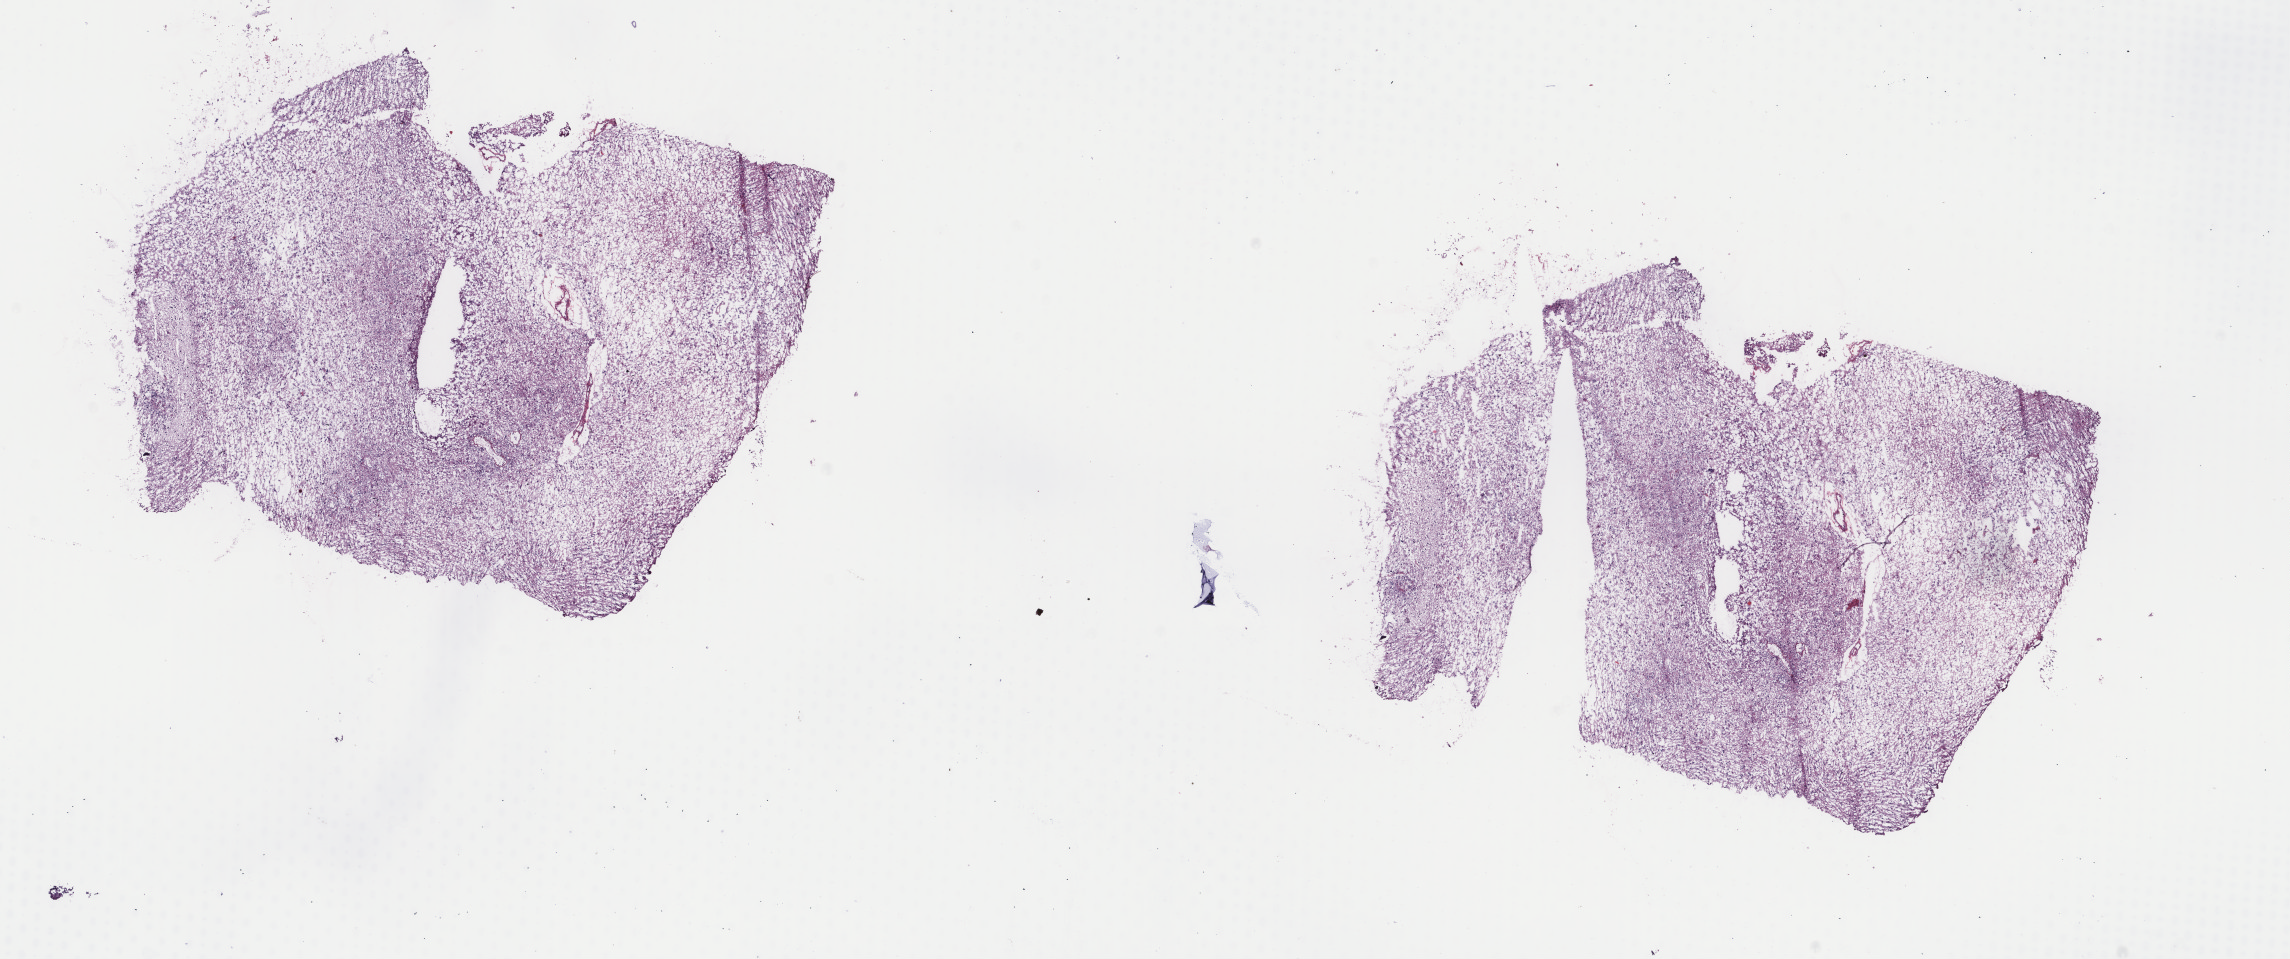
Whole-slide histology image, H&E-stained, shown as a low-resolution overview of the whole scanned area (about 18.2 x 7.6 mm); frozen section from the top of the tissue portion; recurrent tumour sample from the brain. Patient: female, age at initial diagnosis 39 years.
This section: recurrent tumour. Patient diagnosis: Mixed glioma (cerebrum).